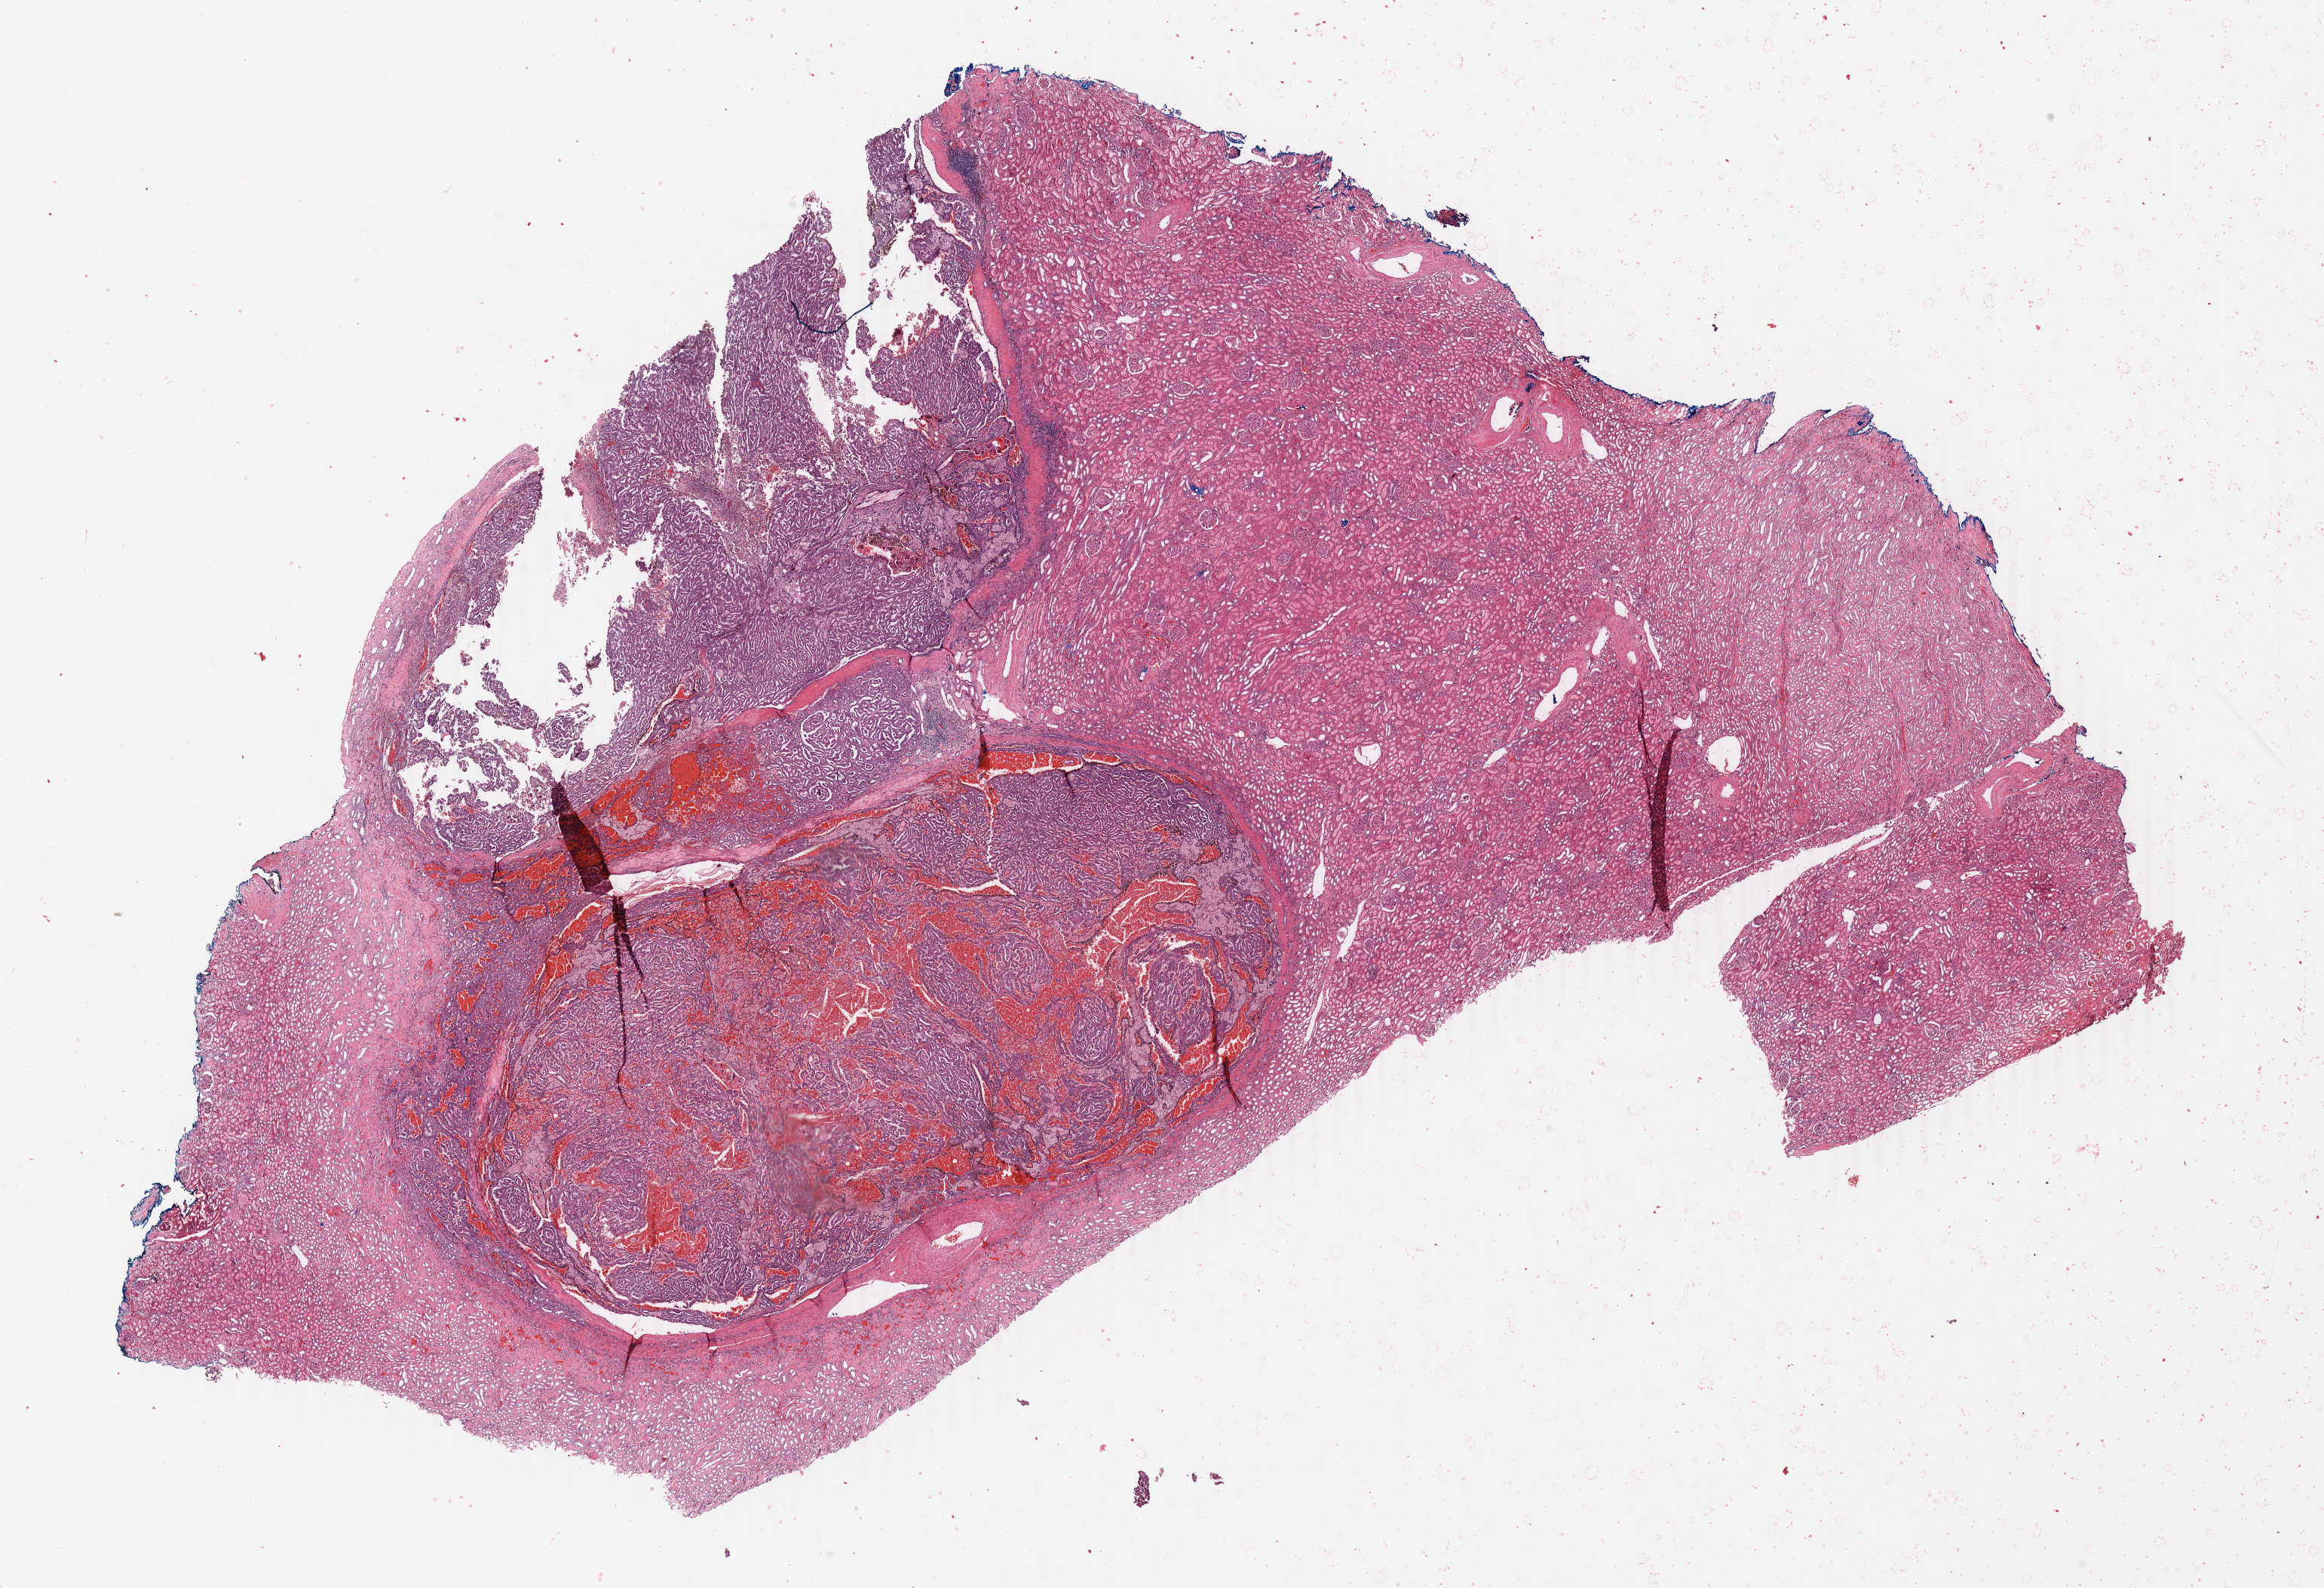
Digitized H&E-stained tissue section (whole slide) — a low-resolution overview of the entire scanned area, about 24.5 x 16.7 mm (acquisition: 40x scan); formalin-fixed paraffin-embedded (FFPE) diagnostic section; sample: primary tumour, kidney. Male patient; age at initial diagnosis 63 years.
Pathologic diagnosis: Papillary adenocarcinoma, NOS. AJCC pathologic stage: I (7th edition).